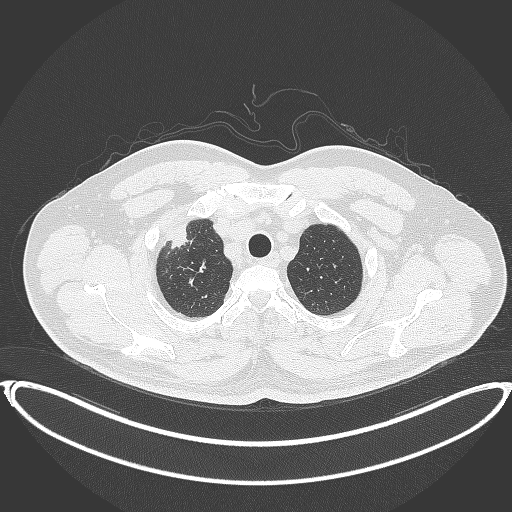
Chest CT, one axial slice. 120 kVp. Lung window (W 1500 / L -600 HU). 1 mm slice thickness. 512 × 512 image matrix. Patient: male, 53 years. Case-level facts recorded for this patient, not image findings: clinical TNM (as recorded): T2a N0 M0.
Outlined on this slice (bounding box drawn by a radiologist):
- lung tumour (recorded histology: adenocarcinoma): bounding box (x1, y1, x2, y2) in pixels: (168, 218, 193, 253)